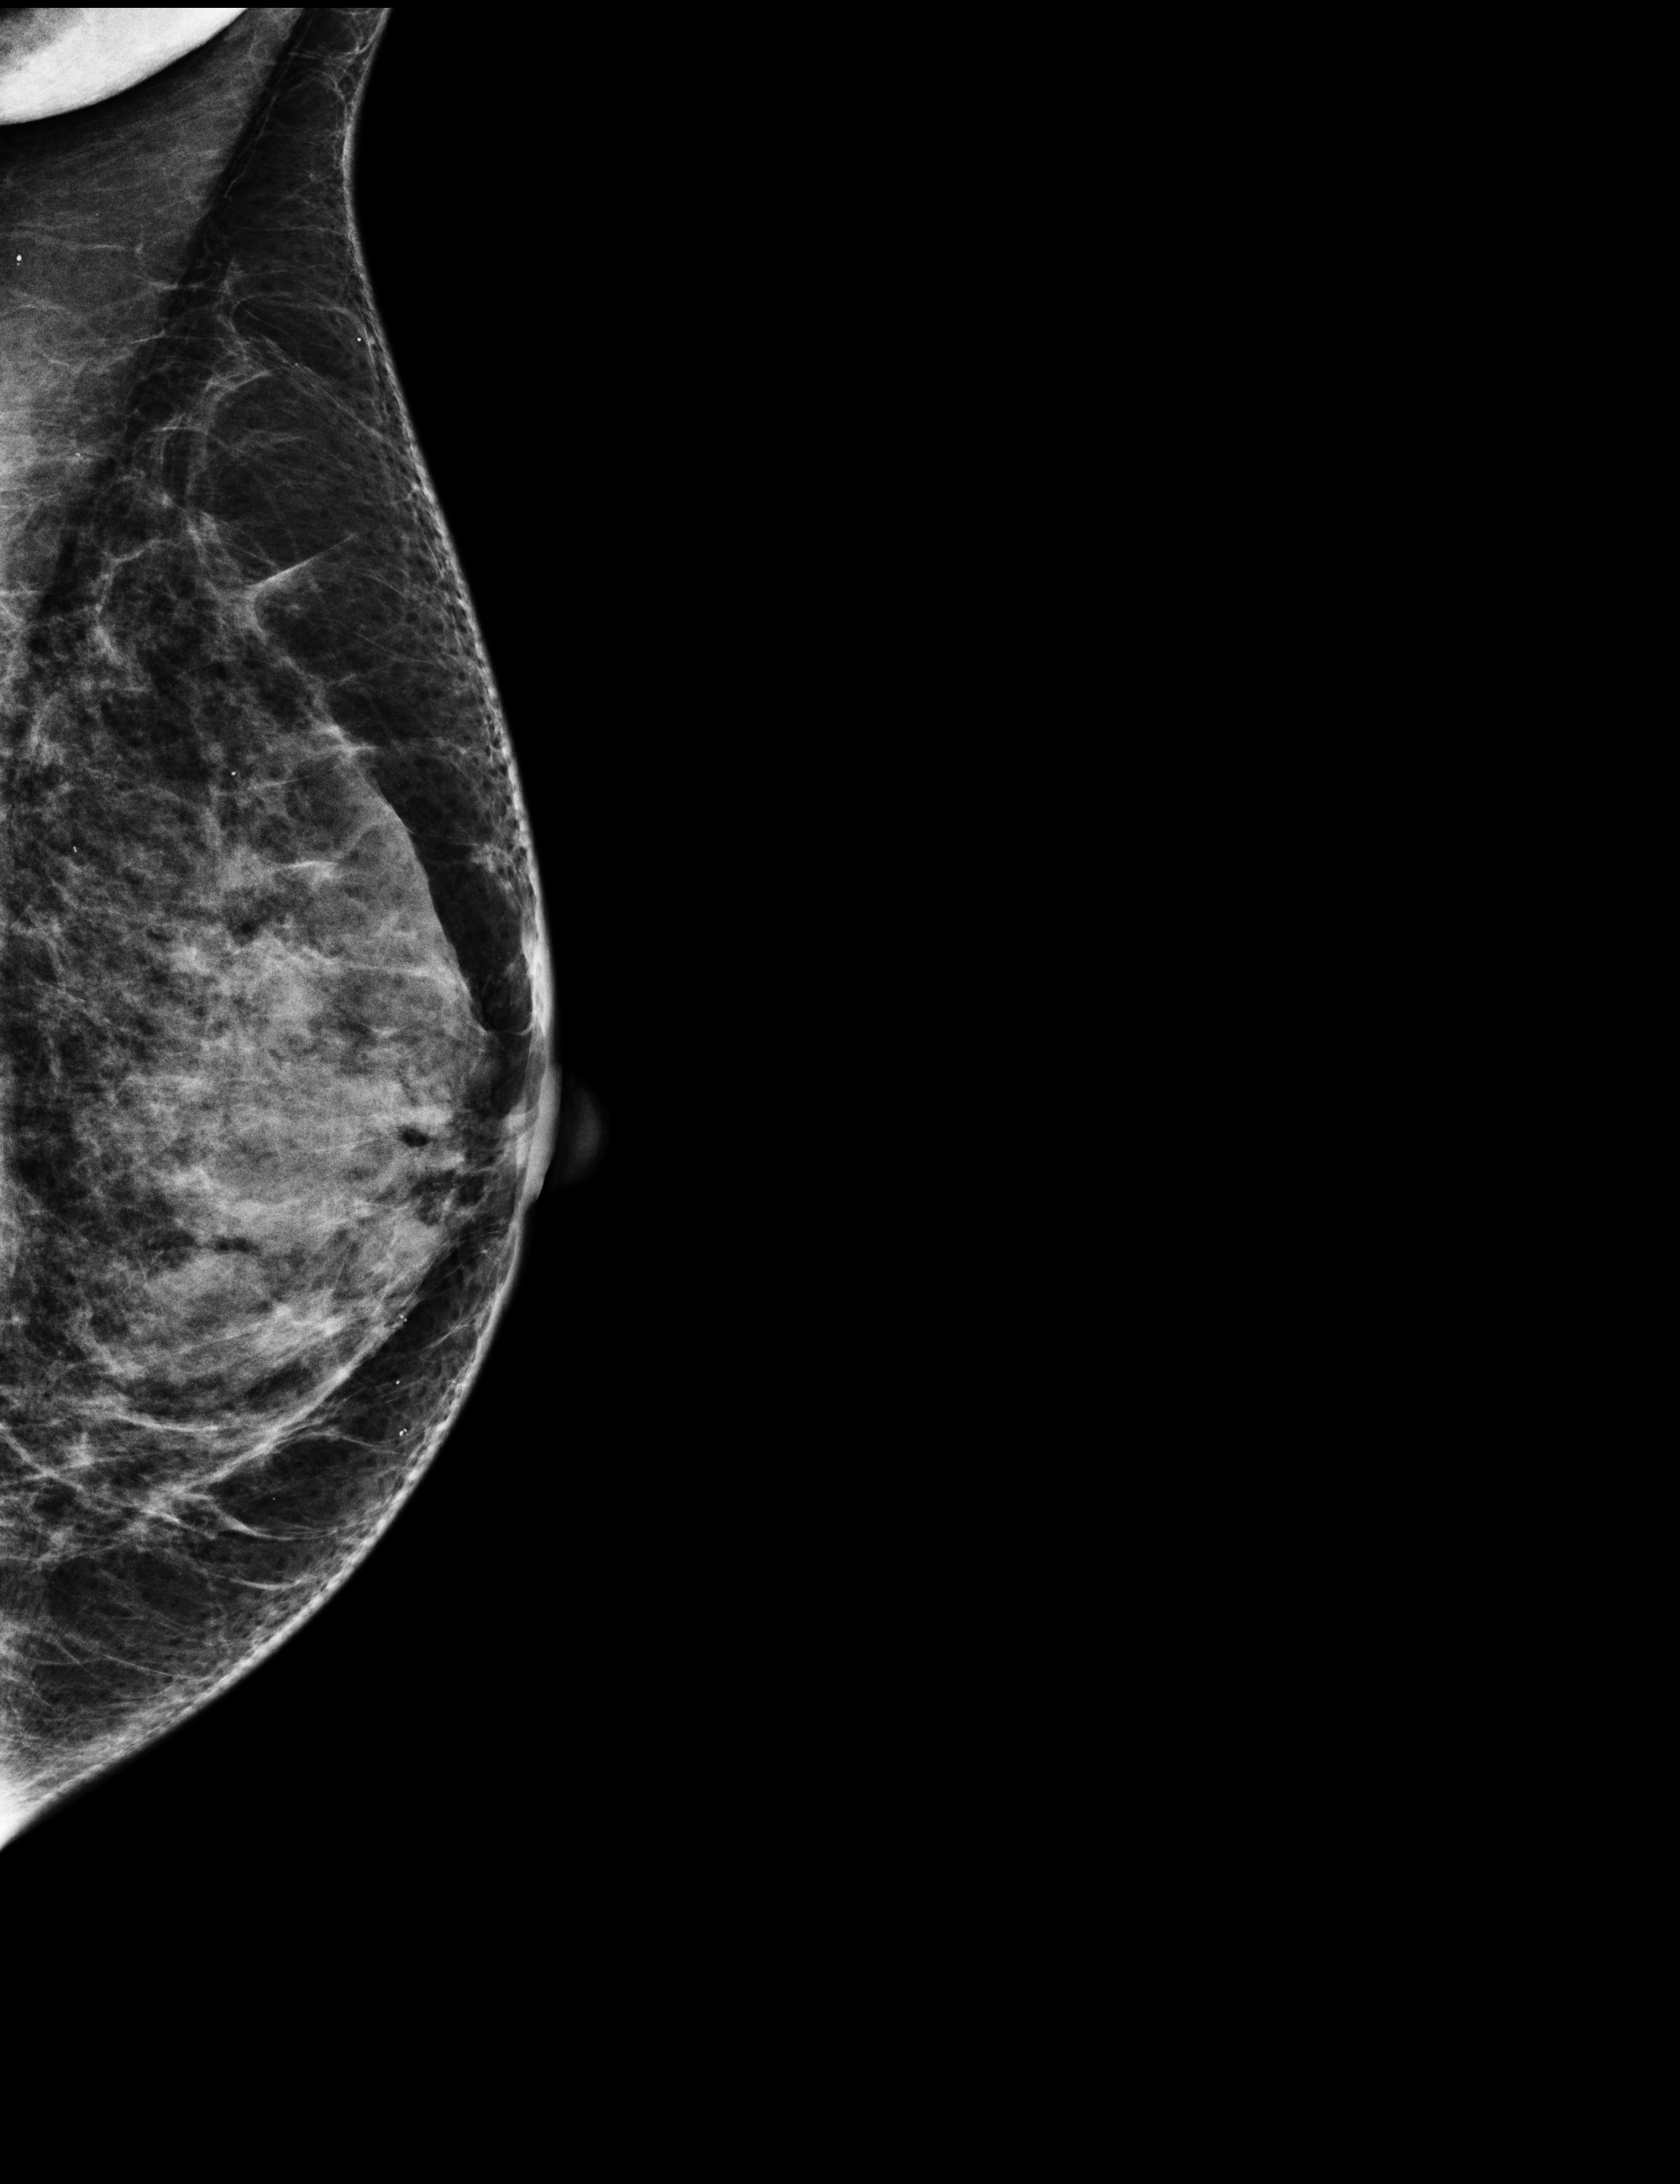
Digital mammogram (FFDM), left breast, MLO view, screening examination, system: Selenia Dimensions. Patient: female, 55 years.
Breast density at the screening exam (both breasts): heterogeneously dense (BI-RADS density category c). Final BI-RADS category for the screening round (tomosynthesis exam, both breasts): category 1. Recall: no recall after this screen.